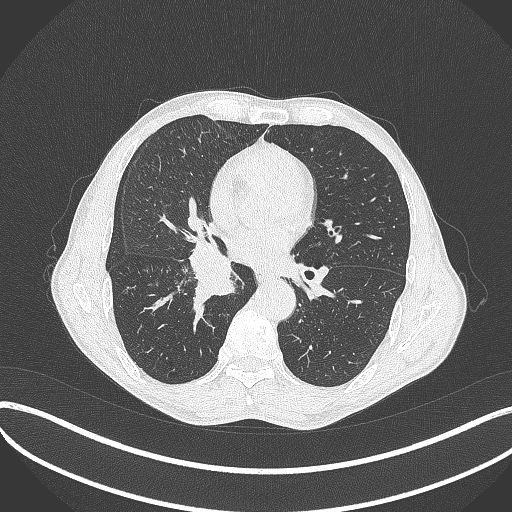
Chest CT, one axial slice; slice 209 of 481 in the series (ordered by position); reconstruction kernel B70f; lung window (W 1500 / L -600 HU); 1 mm slice thickness; 512 × 512 image matrix, field of view 400 × 400 mm. Patient: male, 65 years. Case-level facts recorded for this patient, not image findings: clinical TNM (as recorded): T2a N0 M0; histopathological grade: G2.
Annotated regions visible in this slice (rectangle marked by the reading radiologist):
- lung tumour (recorded histology: squamous cell carcinoma): bounding box (x1, y1, x2, y2) in pixels: (180, 237, 240, 309)